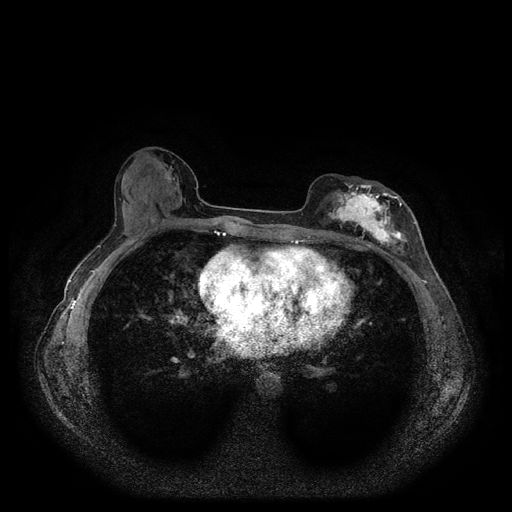
Breast MRI (dynamic contrast-enhanced, multi-phase), one axial slice. Slice 51 of 116 in the series (ordered by position). Dynamic contrast-enhanced series, time point 2 of 5 at this slice position (early post-contrast). 1.5 T. TE 2.6 ms, TR 5.3 ms. 2 mm slice thickness. 512 × 512 image matrix, field of view 350 × 350 mm. Female patient, age 51 years.
Outlined on this slice (semi-automatic segmentation, software-assisted and operator-edited):
- breast lesion (labelled 'tumour' in the annotation; benign lesions carry a separate 'benign' label): bounding box (x1, y1, x2, y2) in pixels: (325, 180, 412, 249)